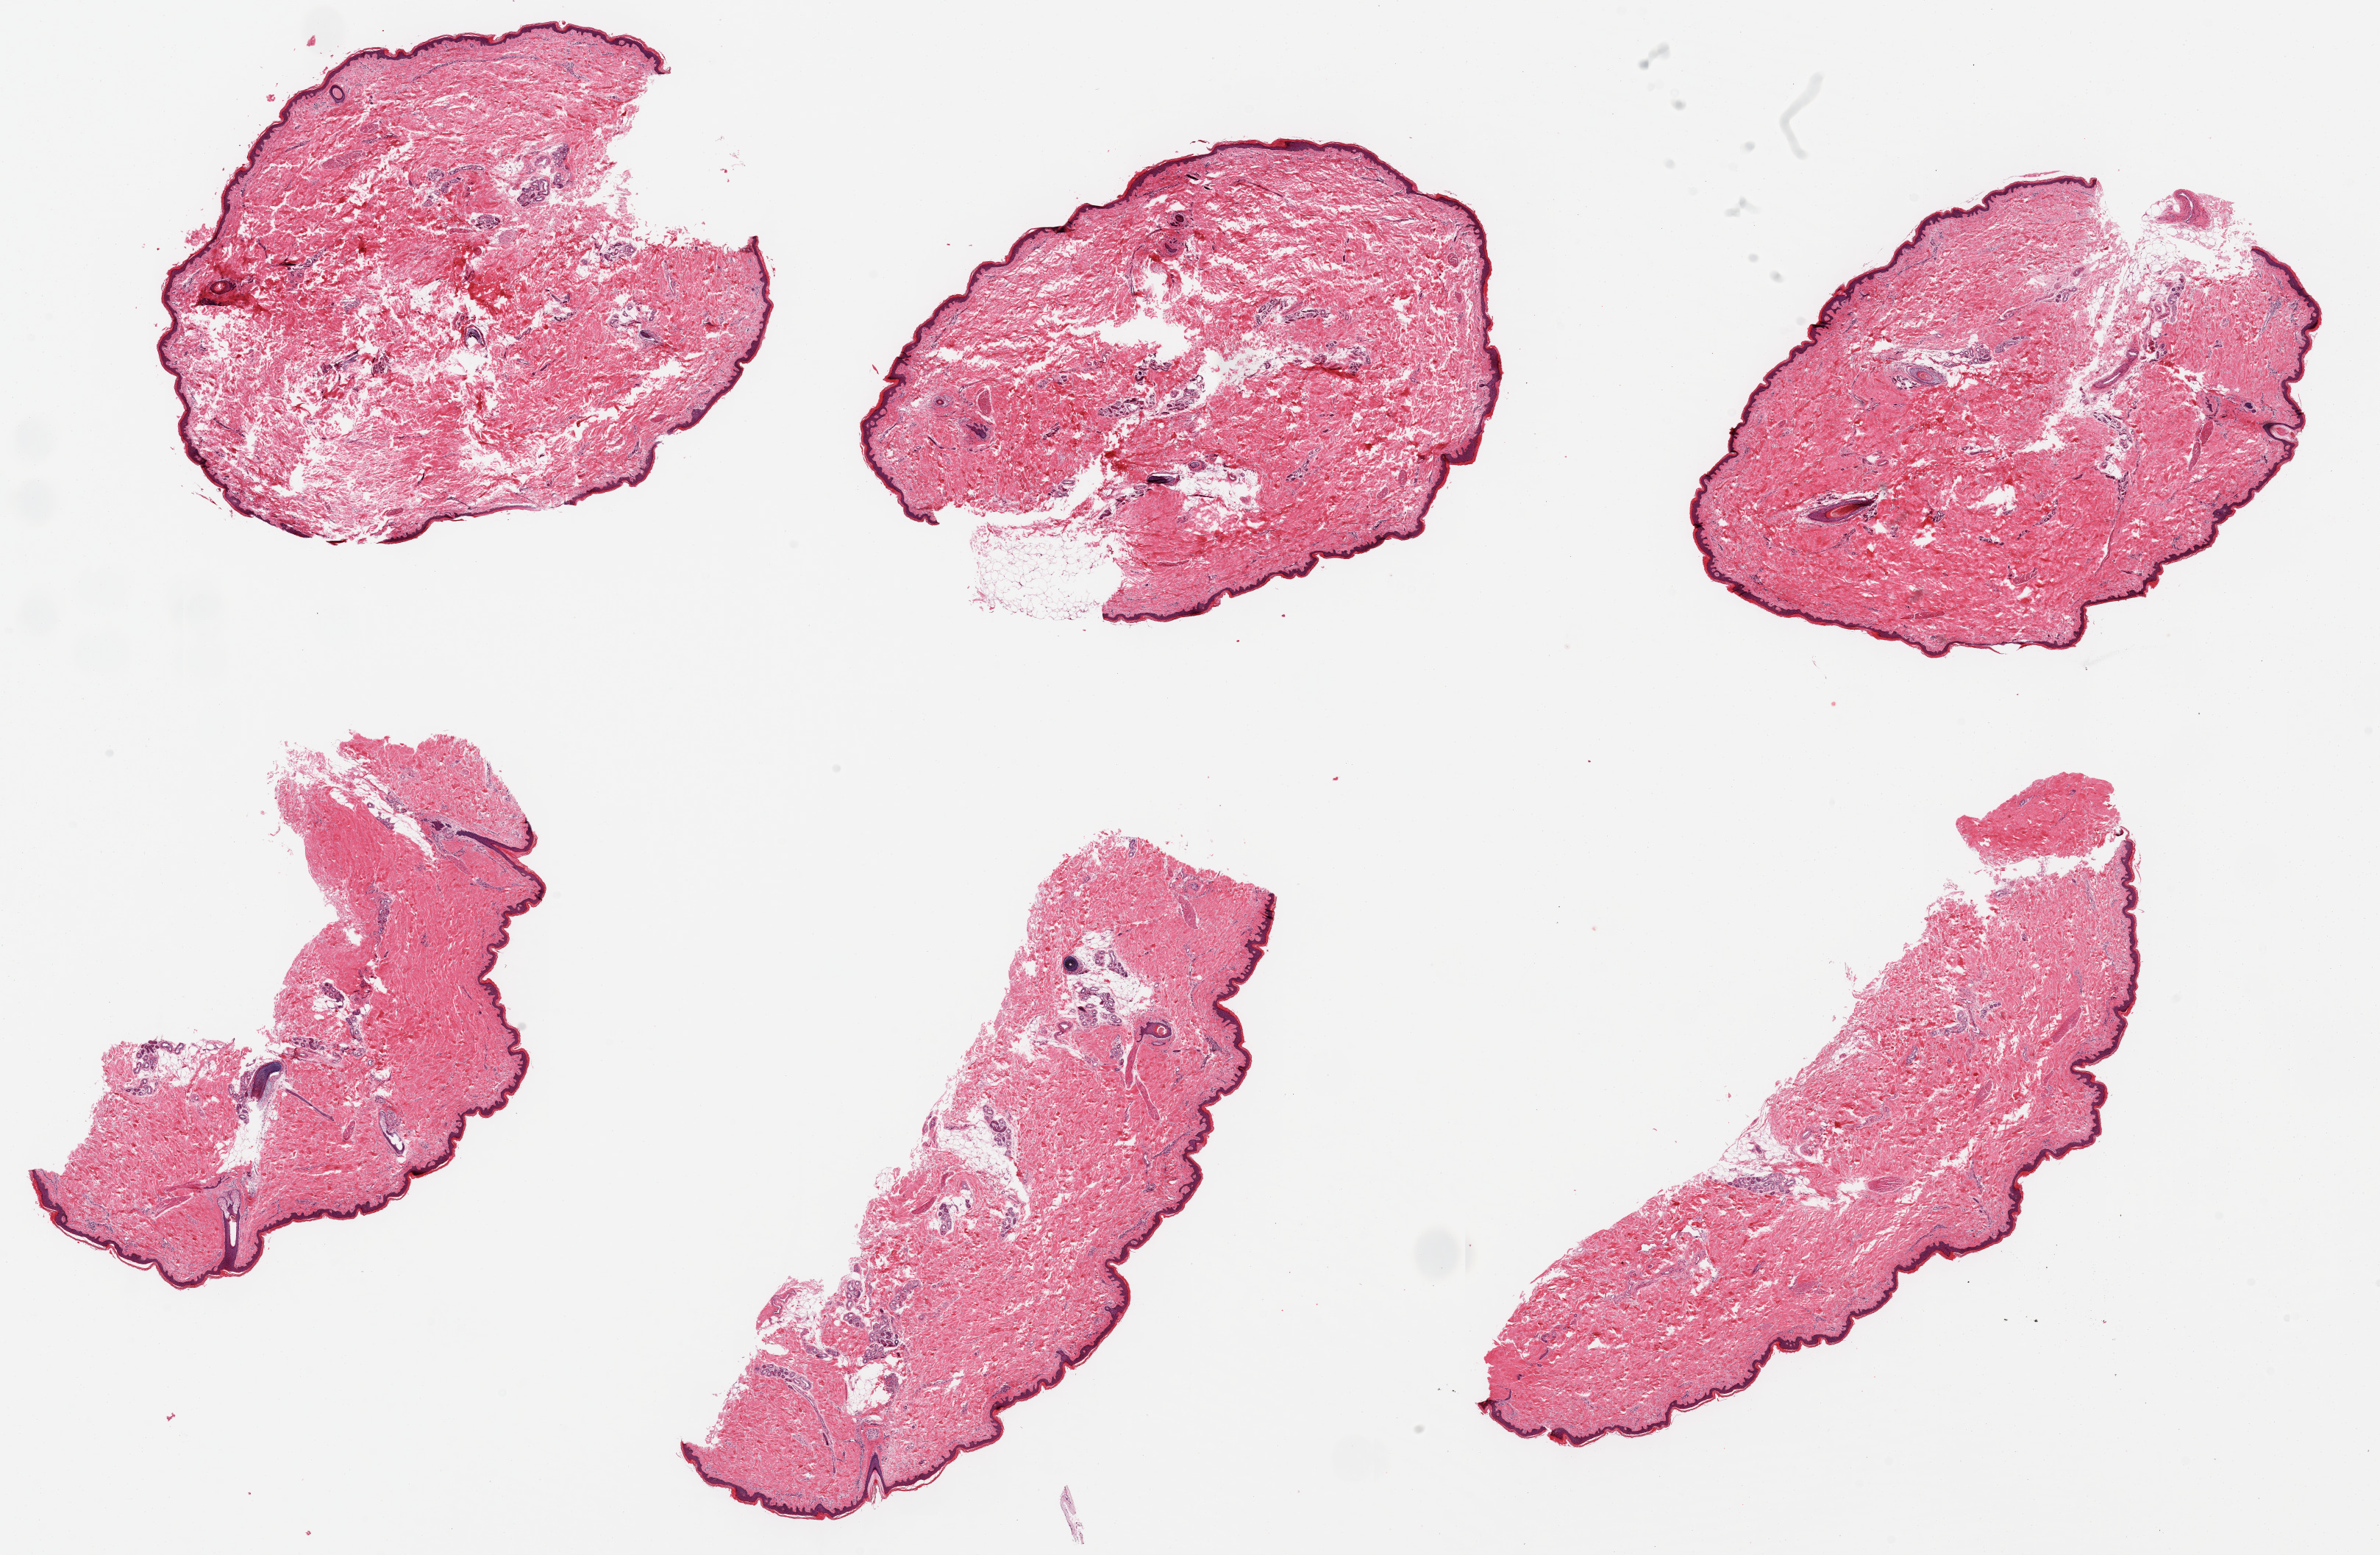
Digitized hematoxylin and eosin (H&E)-stained section — a low-resolution overview of the entire scanned area, about 25.6 x 16.7 mm (from a 20x scan), PAXgene-fixed paraffin-embedded (PFPE) section, target tissue: skin of lower leg, tissue donor sample. Male donor.
• reviewer comment on this tissue sample: 6 pieces up to 9x3 mm; minimal subcutaneous adipose